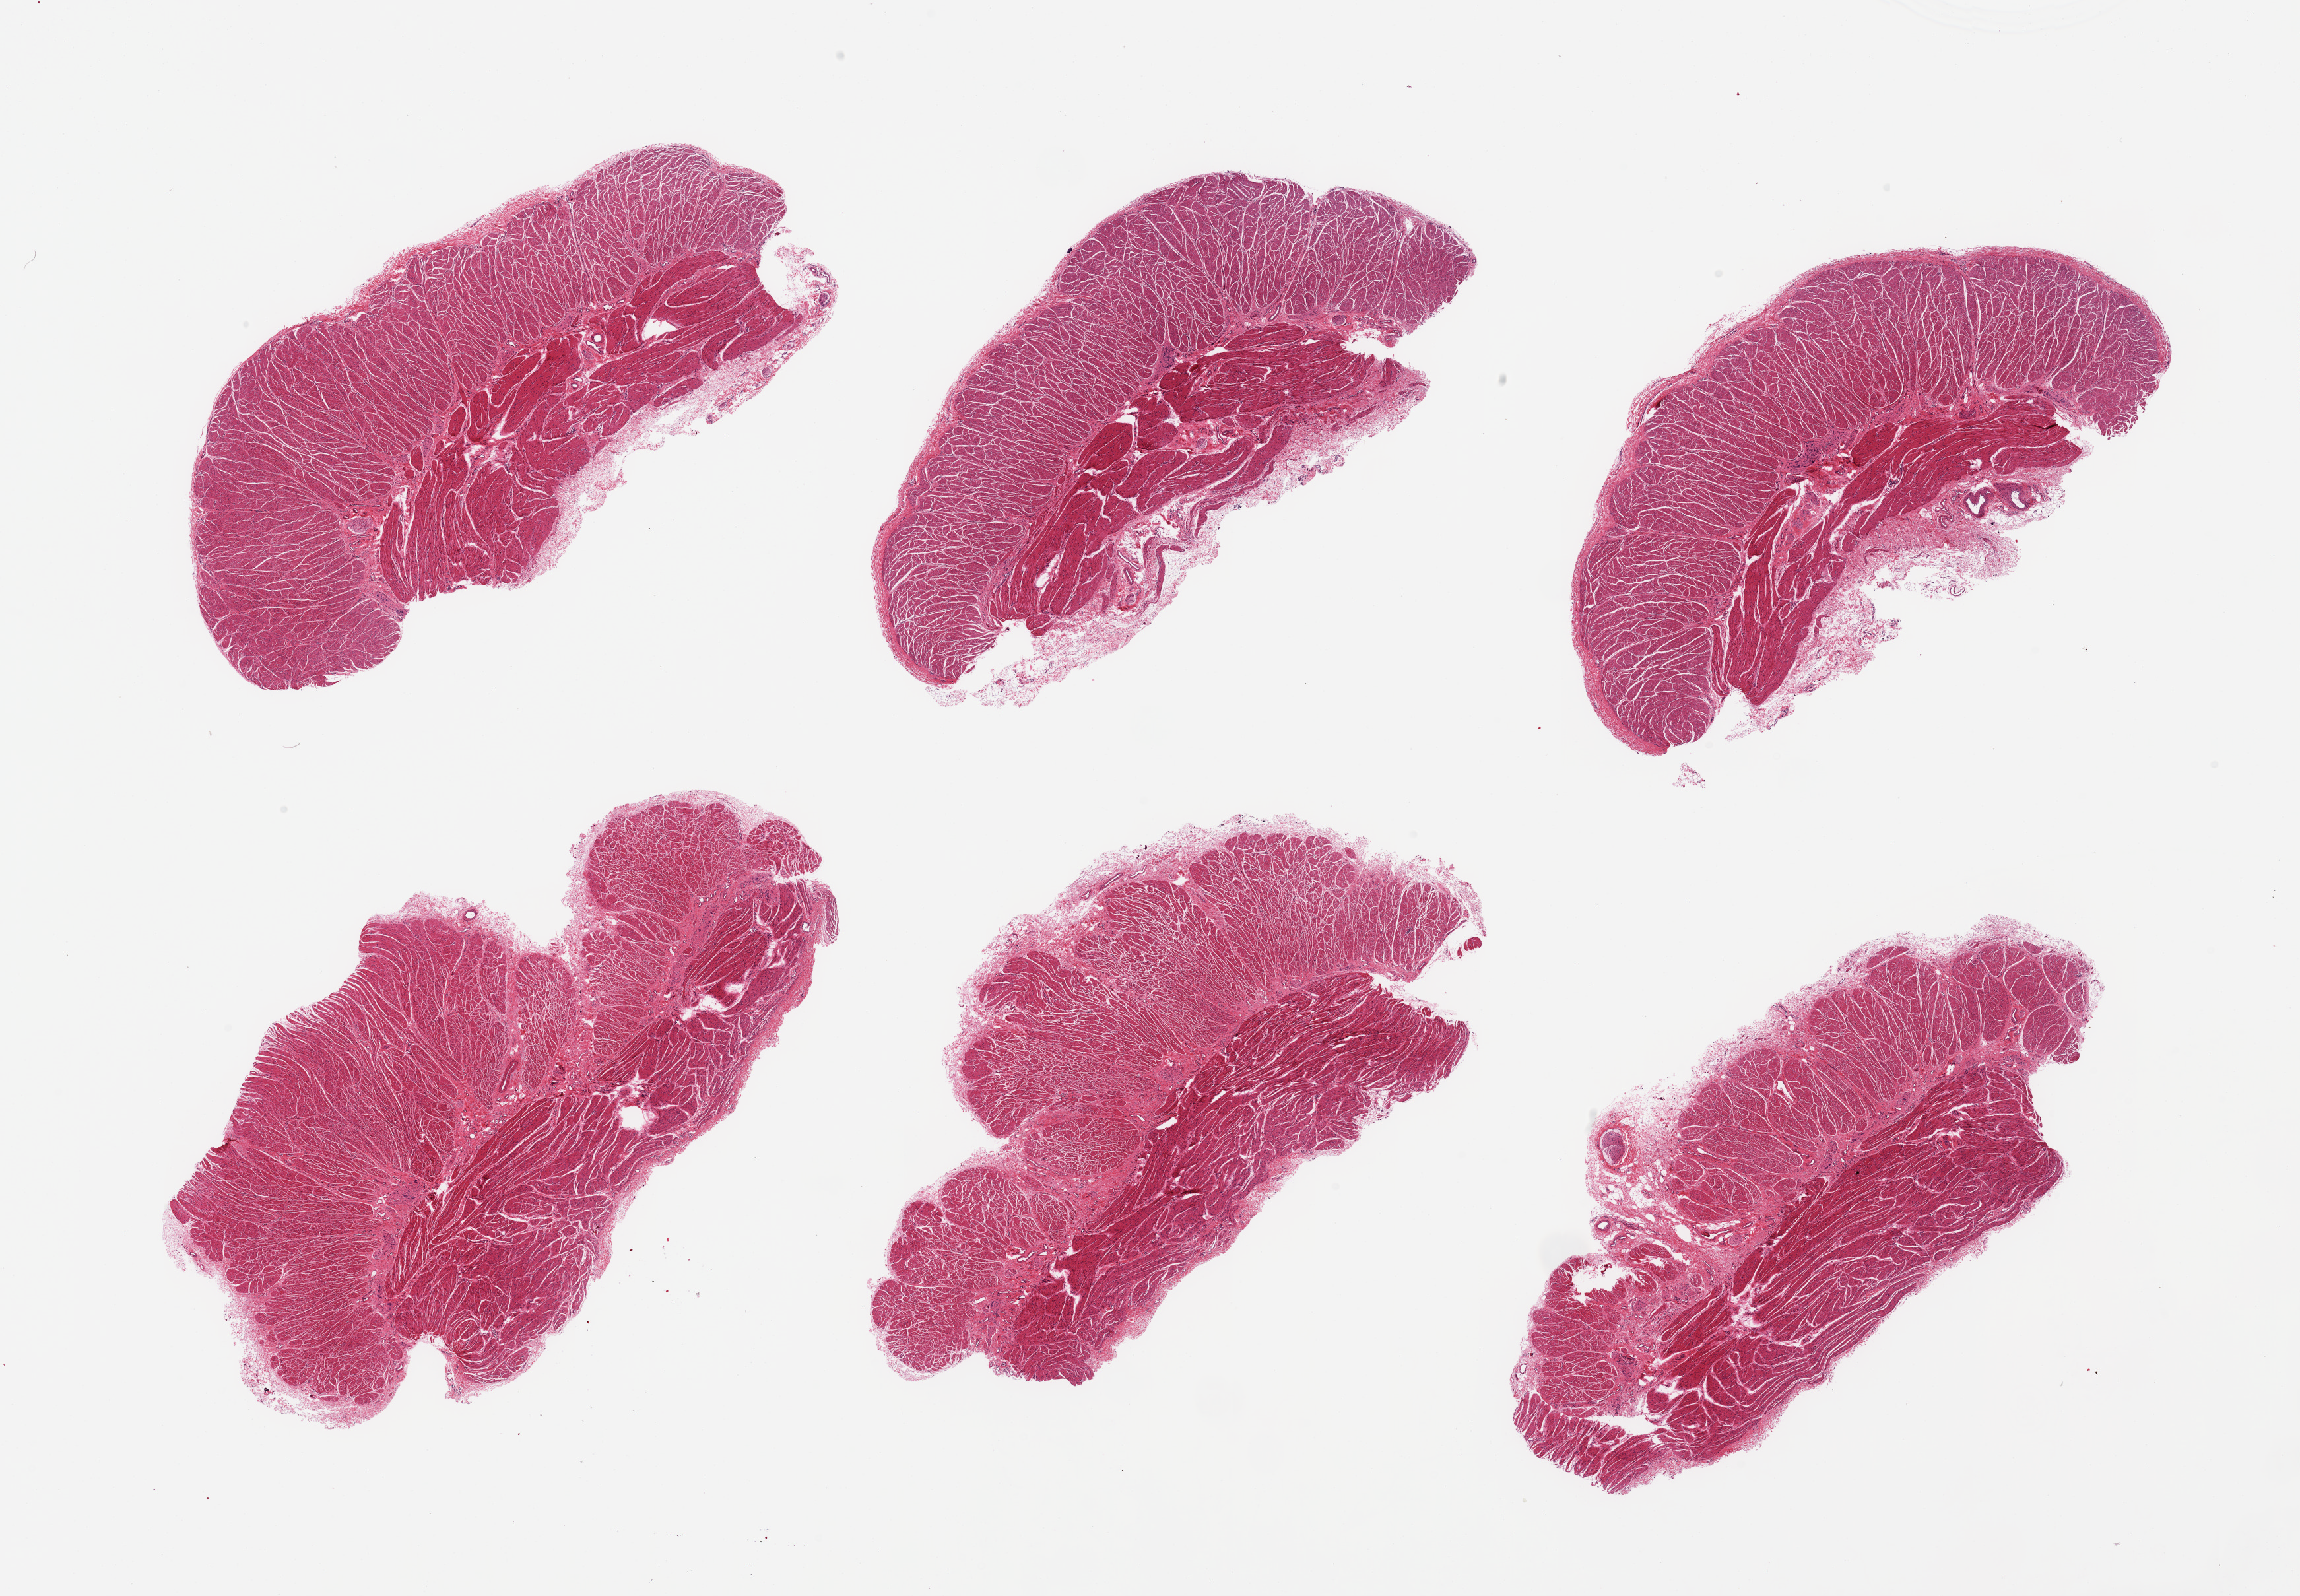
Digitized H&E-stained section, brightfield, low-resolution overview of the scanned area, about 27.6 x 19.1 mm (acquisition: 20x scan), PAXgene-fixed paraffin-embedded (PFPE) section, target tissue: esophageal muscle, tissue donor sample.
Reviewer comment on this tissue sample: 6 piece; essentially well trimmed with a narrow rim of serosa.